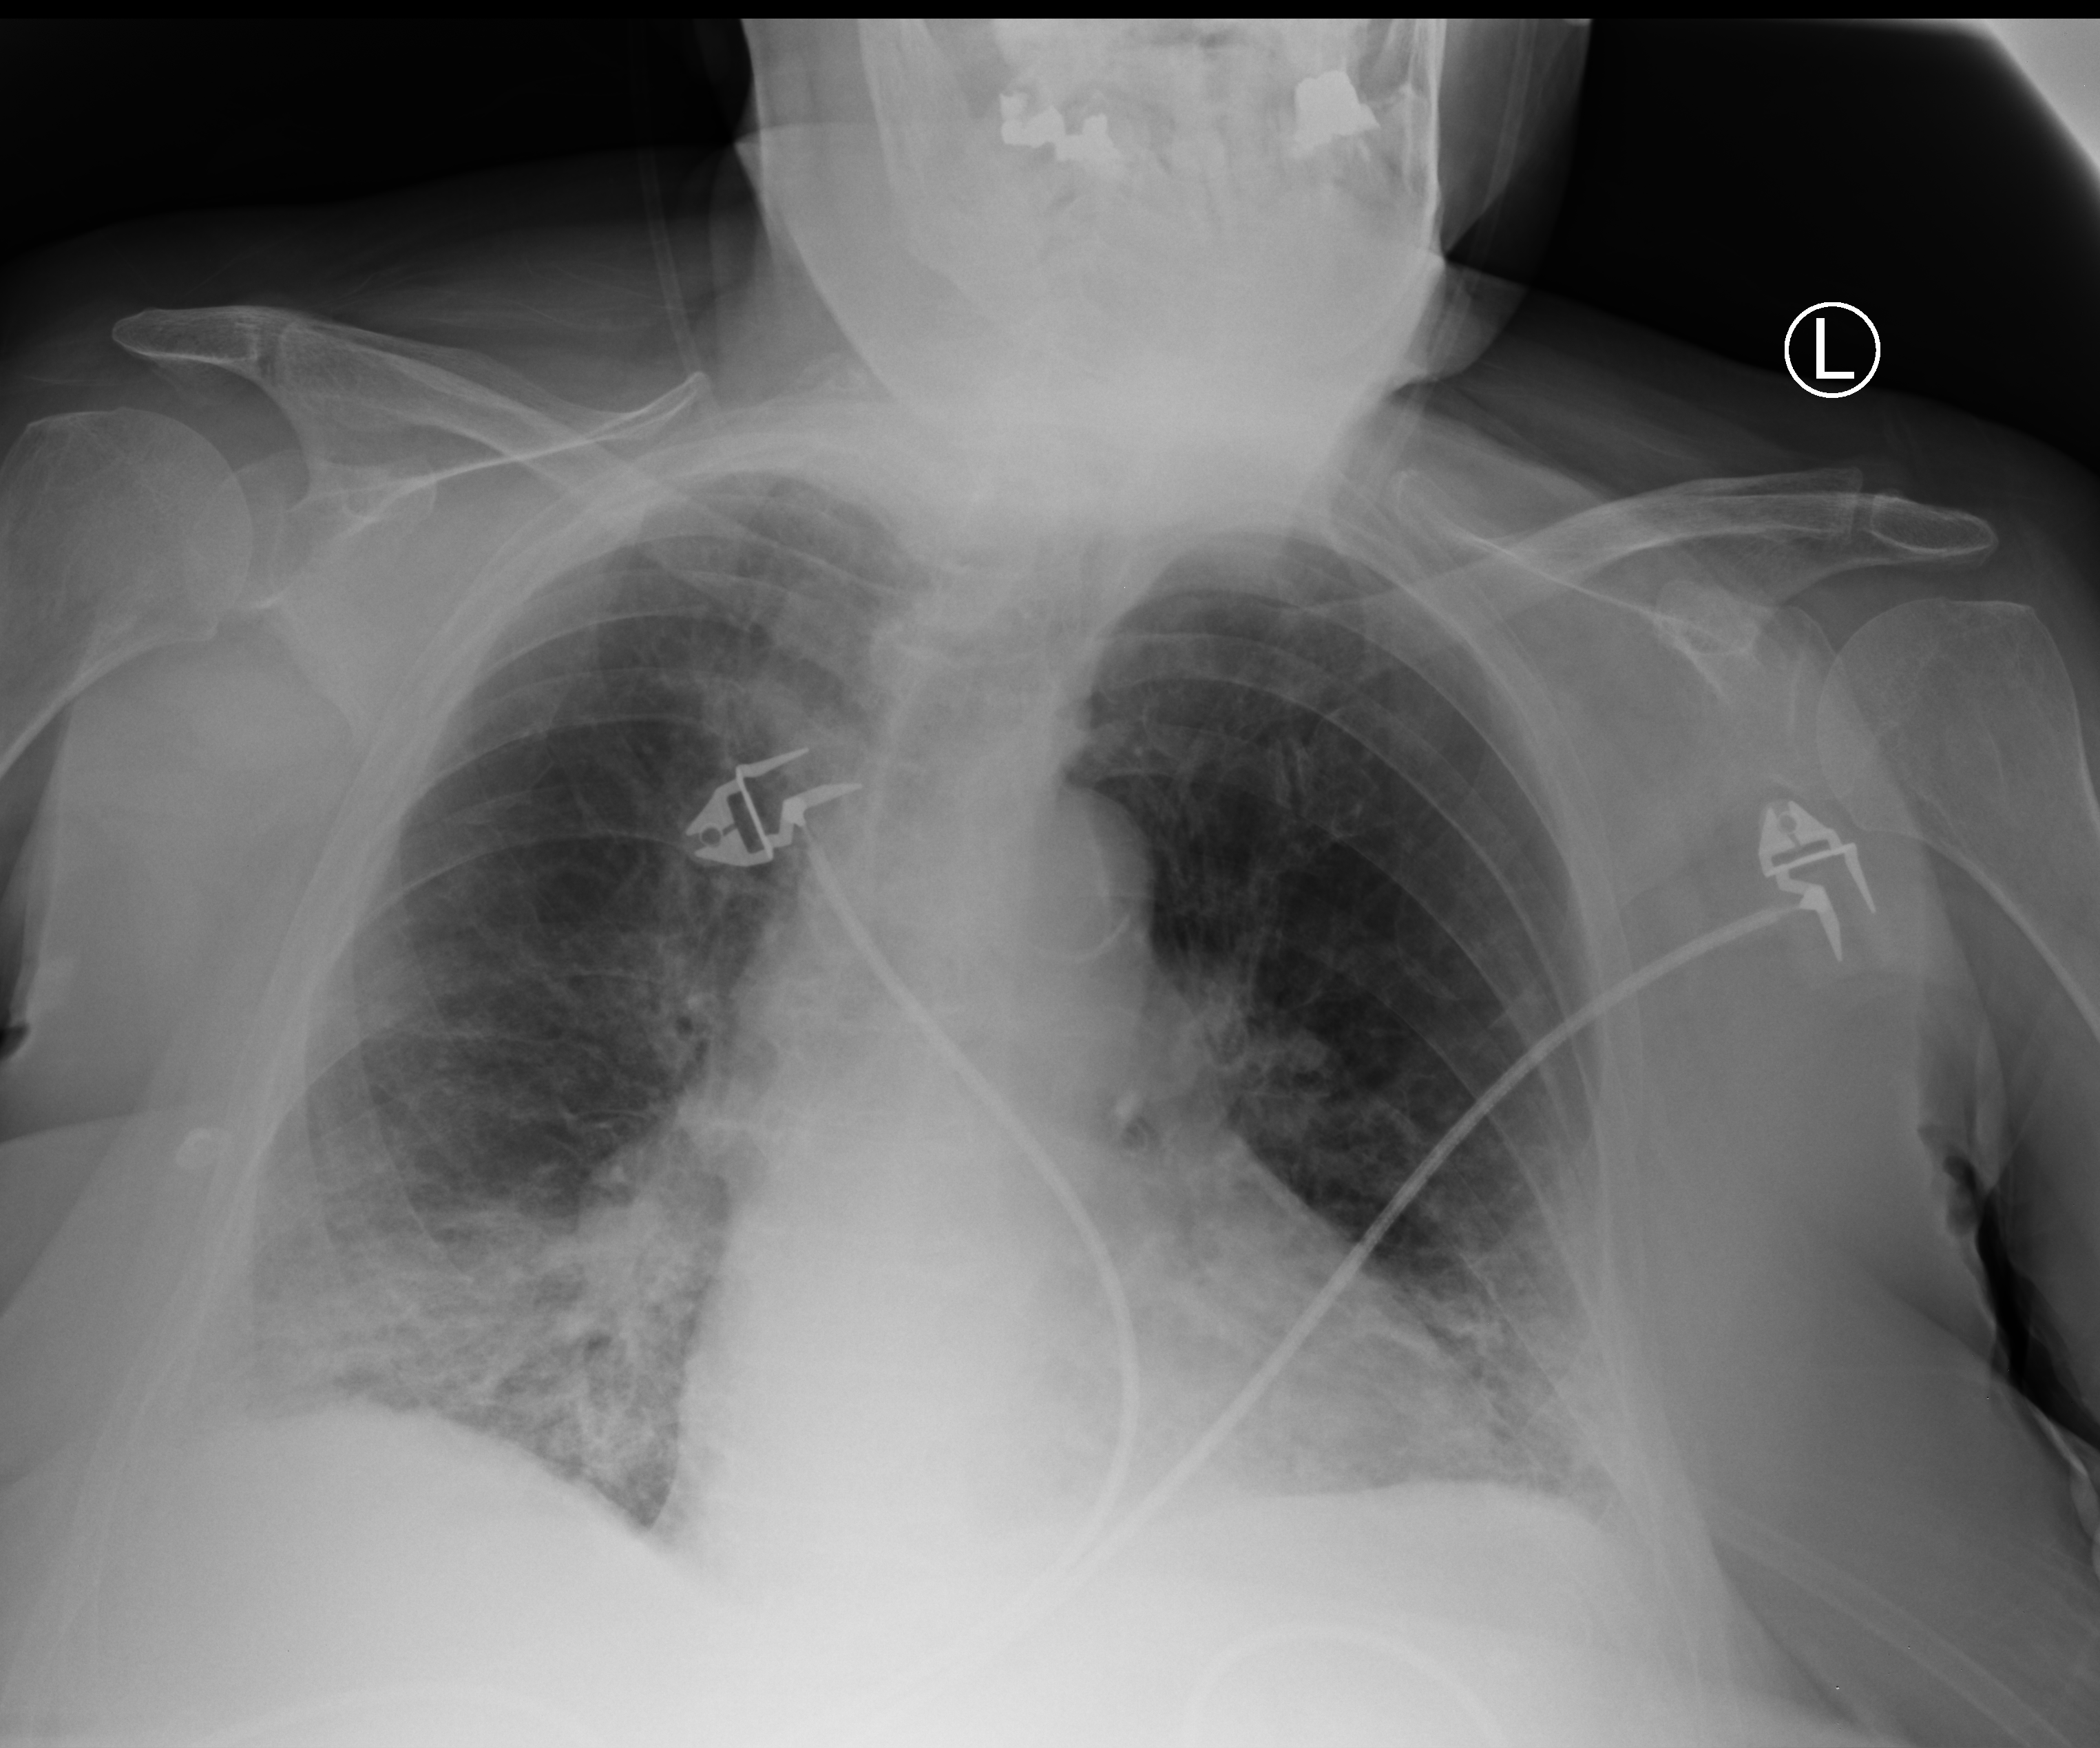
Bedside chest radiograph (computed radiography); anteroposterior (AP) projection. Patient hospitalised with COVID-19; female, aged 75–90 years.
From the hospital-stay record, not from the radiograph (when in the stay this image was taken is not recorded):
- mechanically ventilated during this hospital stay: no
- length of hospital stay: 19 days